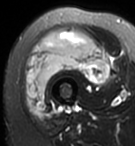
MRI of an extremity soft-tissue mass, one axial slice. Position 33 of 95 along the scan axis. T2-weighted fat-saturated. MR volume resampled by the dataset authors to the PET/CT grid (not the native acquisition matrix). 135 × 146 image matrix. Female patient. From the clinical record (not read from this slice): histological type: pleiomorphic undifferentiated sarcoma; grade: high; site of the primary tumour: right quadricep.
Annotated regions visible in this slice (expert contour drawn on MRI and transferred to this co-registered scan by the dataset authors):
- gross tumour volume including surrounding oedema: bounding box [x1, y1, x2, y2] px = [25, 29, 109, 115]
- gross tumour volume (mass): [25, 29, 109, 115]